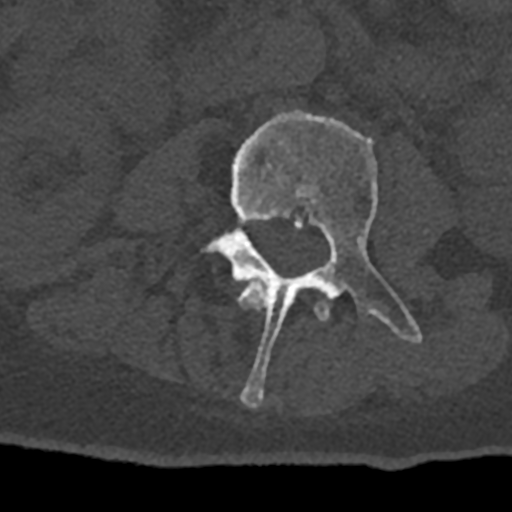
CT including the spine, one axial slice; position 319 of 797 along the scan axis; 120 kVp; bone window (W 1800 / L 400 HU); 0.5 mm slice thickness; 512 × 512 image matrix, field of view 160 × 160 mm. Patient: male, 74 years. From the clinical record (not read from this slice): primary cancer: renal; vertebrae with lytic lesions (as recorded): T10, L1, L2, L3, L4, L5.
Outlined on this slice (semi-automatically segmented with operator editing):
- L2 vertebra: bounding box <237,280,329,321> (left, top, right, bottom; pixels)
- L3 vertebra: <201,109,423,408>